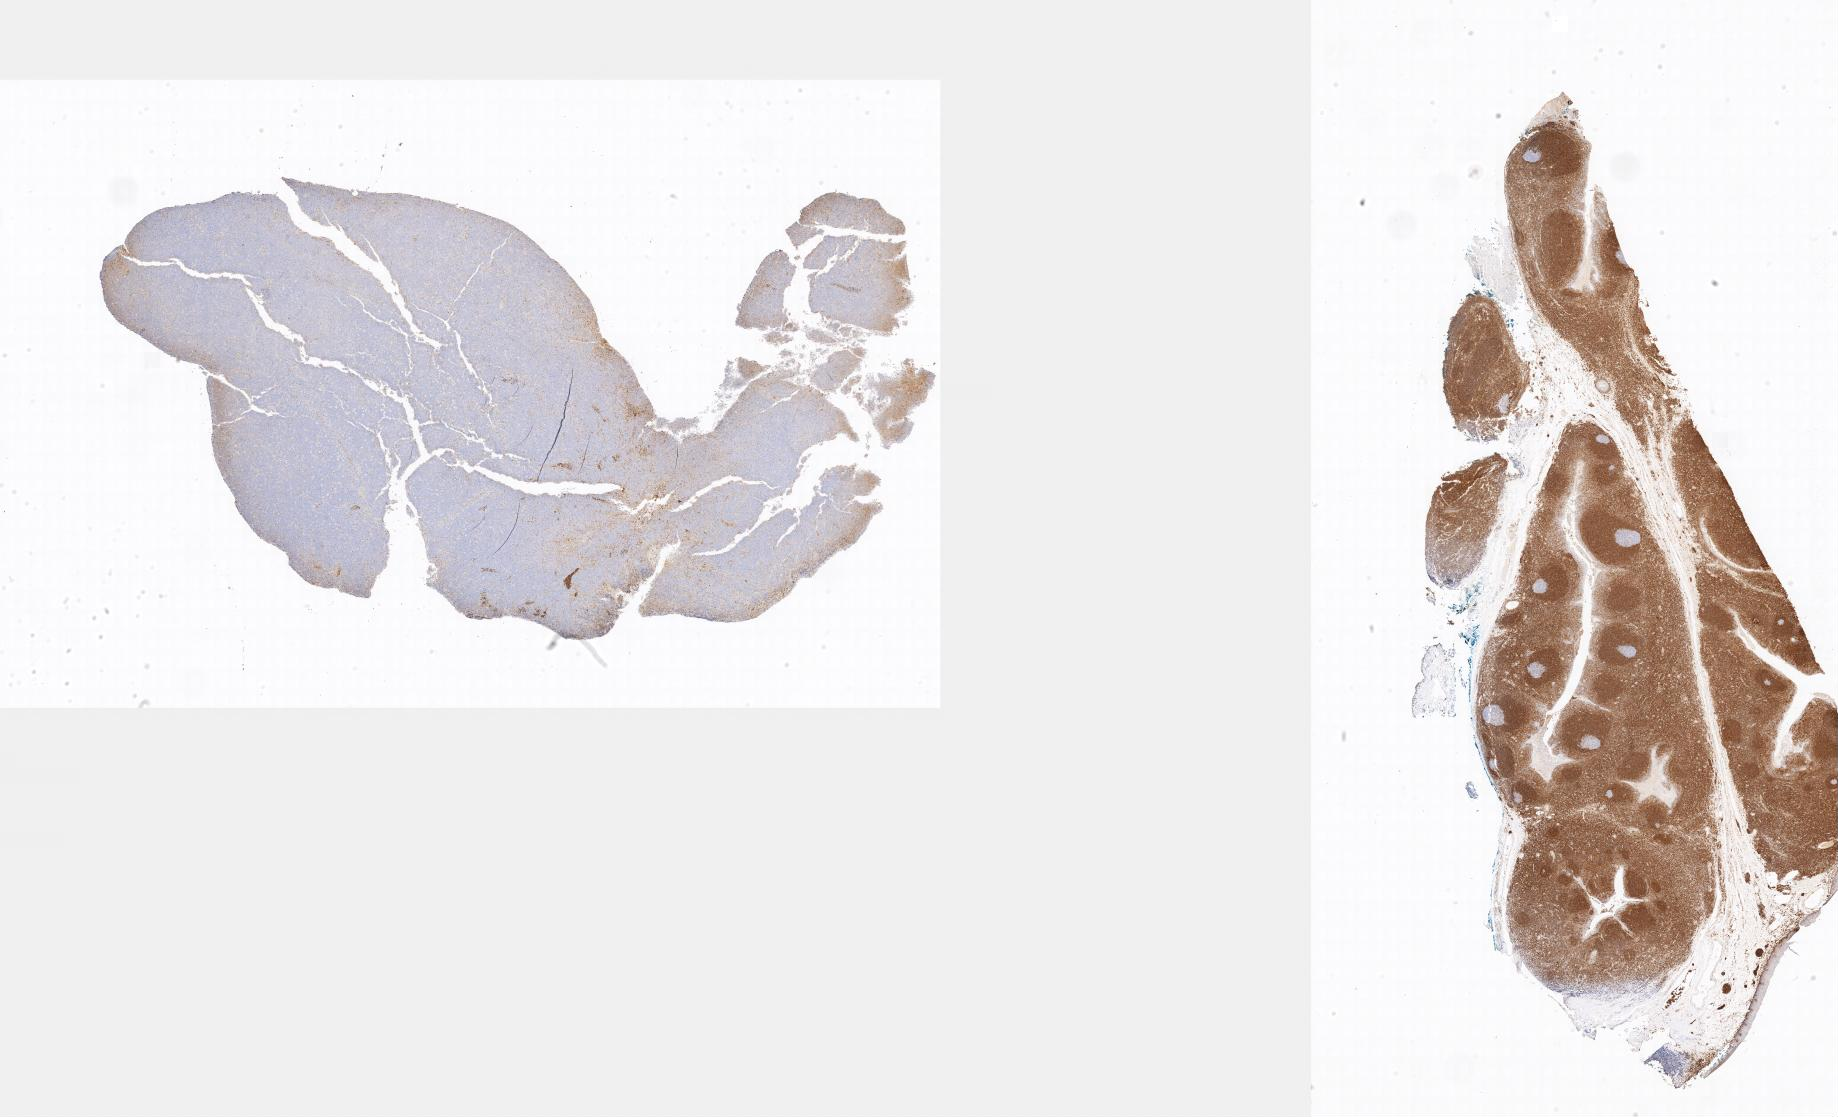
Whole-slide image, immunohistochemical stain for BCL2, a low-resolution overview of the entire scanned area. Tumor tissue. Site: lymph node of head and neck. Male, age 5 years at initial diagnosis.
Diagnosis: Burkitt lymphoma, NOS.